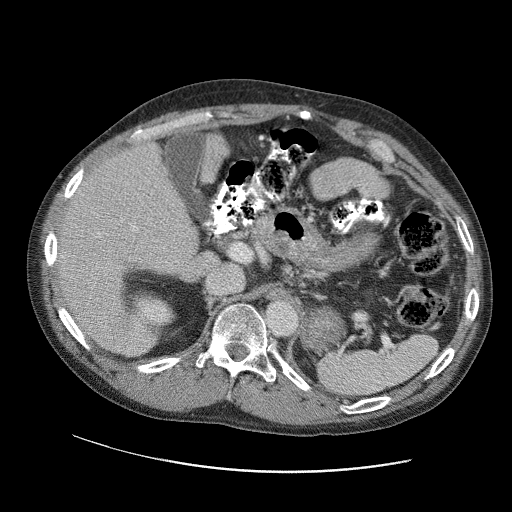
Contrast-enhanced abdominal CT (liver protocol), one axial slice; reconstruction kernel STANDARD; 120 kVp; soft-tissue window (W 400 / L 40 HU); 2.5 mm slice thickness; 512 × 512 image matrix, field of view 400 × 400 mm. Case-level facts recorded for this patient, not image findings: diagnosis: hepatocellular carcinoma (patient treated with transarterial chemoembolisation; whether this scan precedes or follows treatment is not stated here); TNM stage (as recorded): Stage-IIIC; Child-Pugh class: B; tumour differentiation: well differentiated.
Annotated regions visible in this slice (semi-automatically segmented with operator editing):
- liver parenchyma outside the tumour (the mass and vessels are separate outlines, so this box may not span the whole liver): bounding box [x1, y1, x2, y2] px = [52, 142, 198, 350]
- liver vessels: [52, 169, 178, 320]